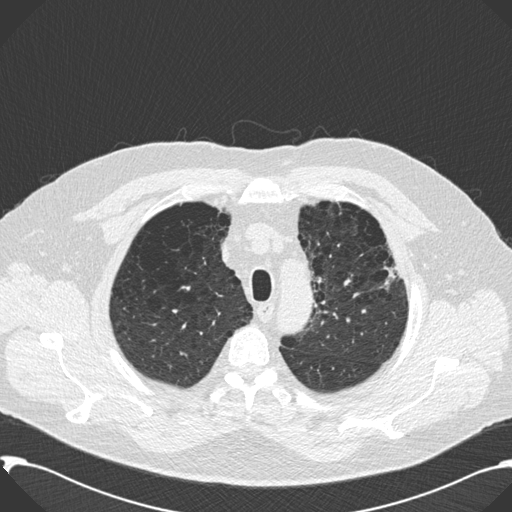
Axial slice from a low-dose chest CT screening exam; second annual screen; lung window (W 1500 / L -600 HU); standard (soft-tissue) reconstruction kernel (B30f); slice 33 of 199 in the series. Male participant, aged 59 years at enrolment. Current smoker at enrolment.
Lesion marked by an expert reader, bounding box (x1, y1, x2, y2) in pixels: (366, 241, 410, 304). No non-calcified nodule or mass ≥4 mm was recorded by the screening reader at this exam. Participant outcome: lung cancer diagnosed 518 days after this screen (after the third annual screen) — bronchiolo-alveolar carcinoma, mixed mucinous and non-mucinous, left upper lobe, stage IA (AJCC 6th edition), 20 mm at pathology.